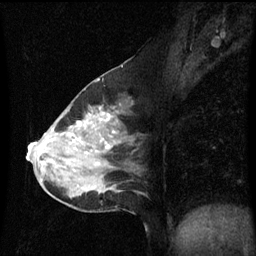
Breast MRI (dynamic contrast-enhanced), one sagittal slice; slice 32 of 60 in the series (ordered by position); dynamic contrast-enhanced series, image 2 of 3 at this slice position (ordered by acquisition); 1.5 T; TE 4.2 ms, TR 8.9 ms; 2 mm slice thickness; 256 × 256 image matrix. Patient: female, 50 years. From the clinical record (not read from this slice): setting: breast cancer imaged before/during neoadjuvant chemotherapy; receptor status: HR-positive, HER2-negative.
Annotated regions visible in this slice (semi-automatic segmentation, software-assisted and operator-edited):
- analysis volume of interest (the breast-tissue region the enhancement analysis was run in; not a lesion): bounding box <33,90,137,209> (left, top, right, bottom; pixels)
- tumour enhancement mask (voxels above the 70 % enhancement threshold inside the analysis volume of interest): <33,114,111,149>